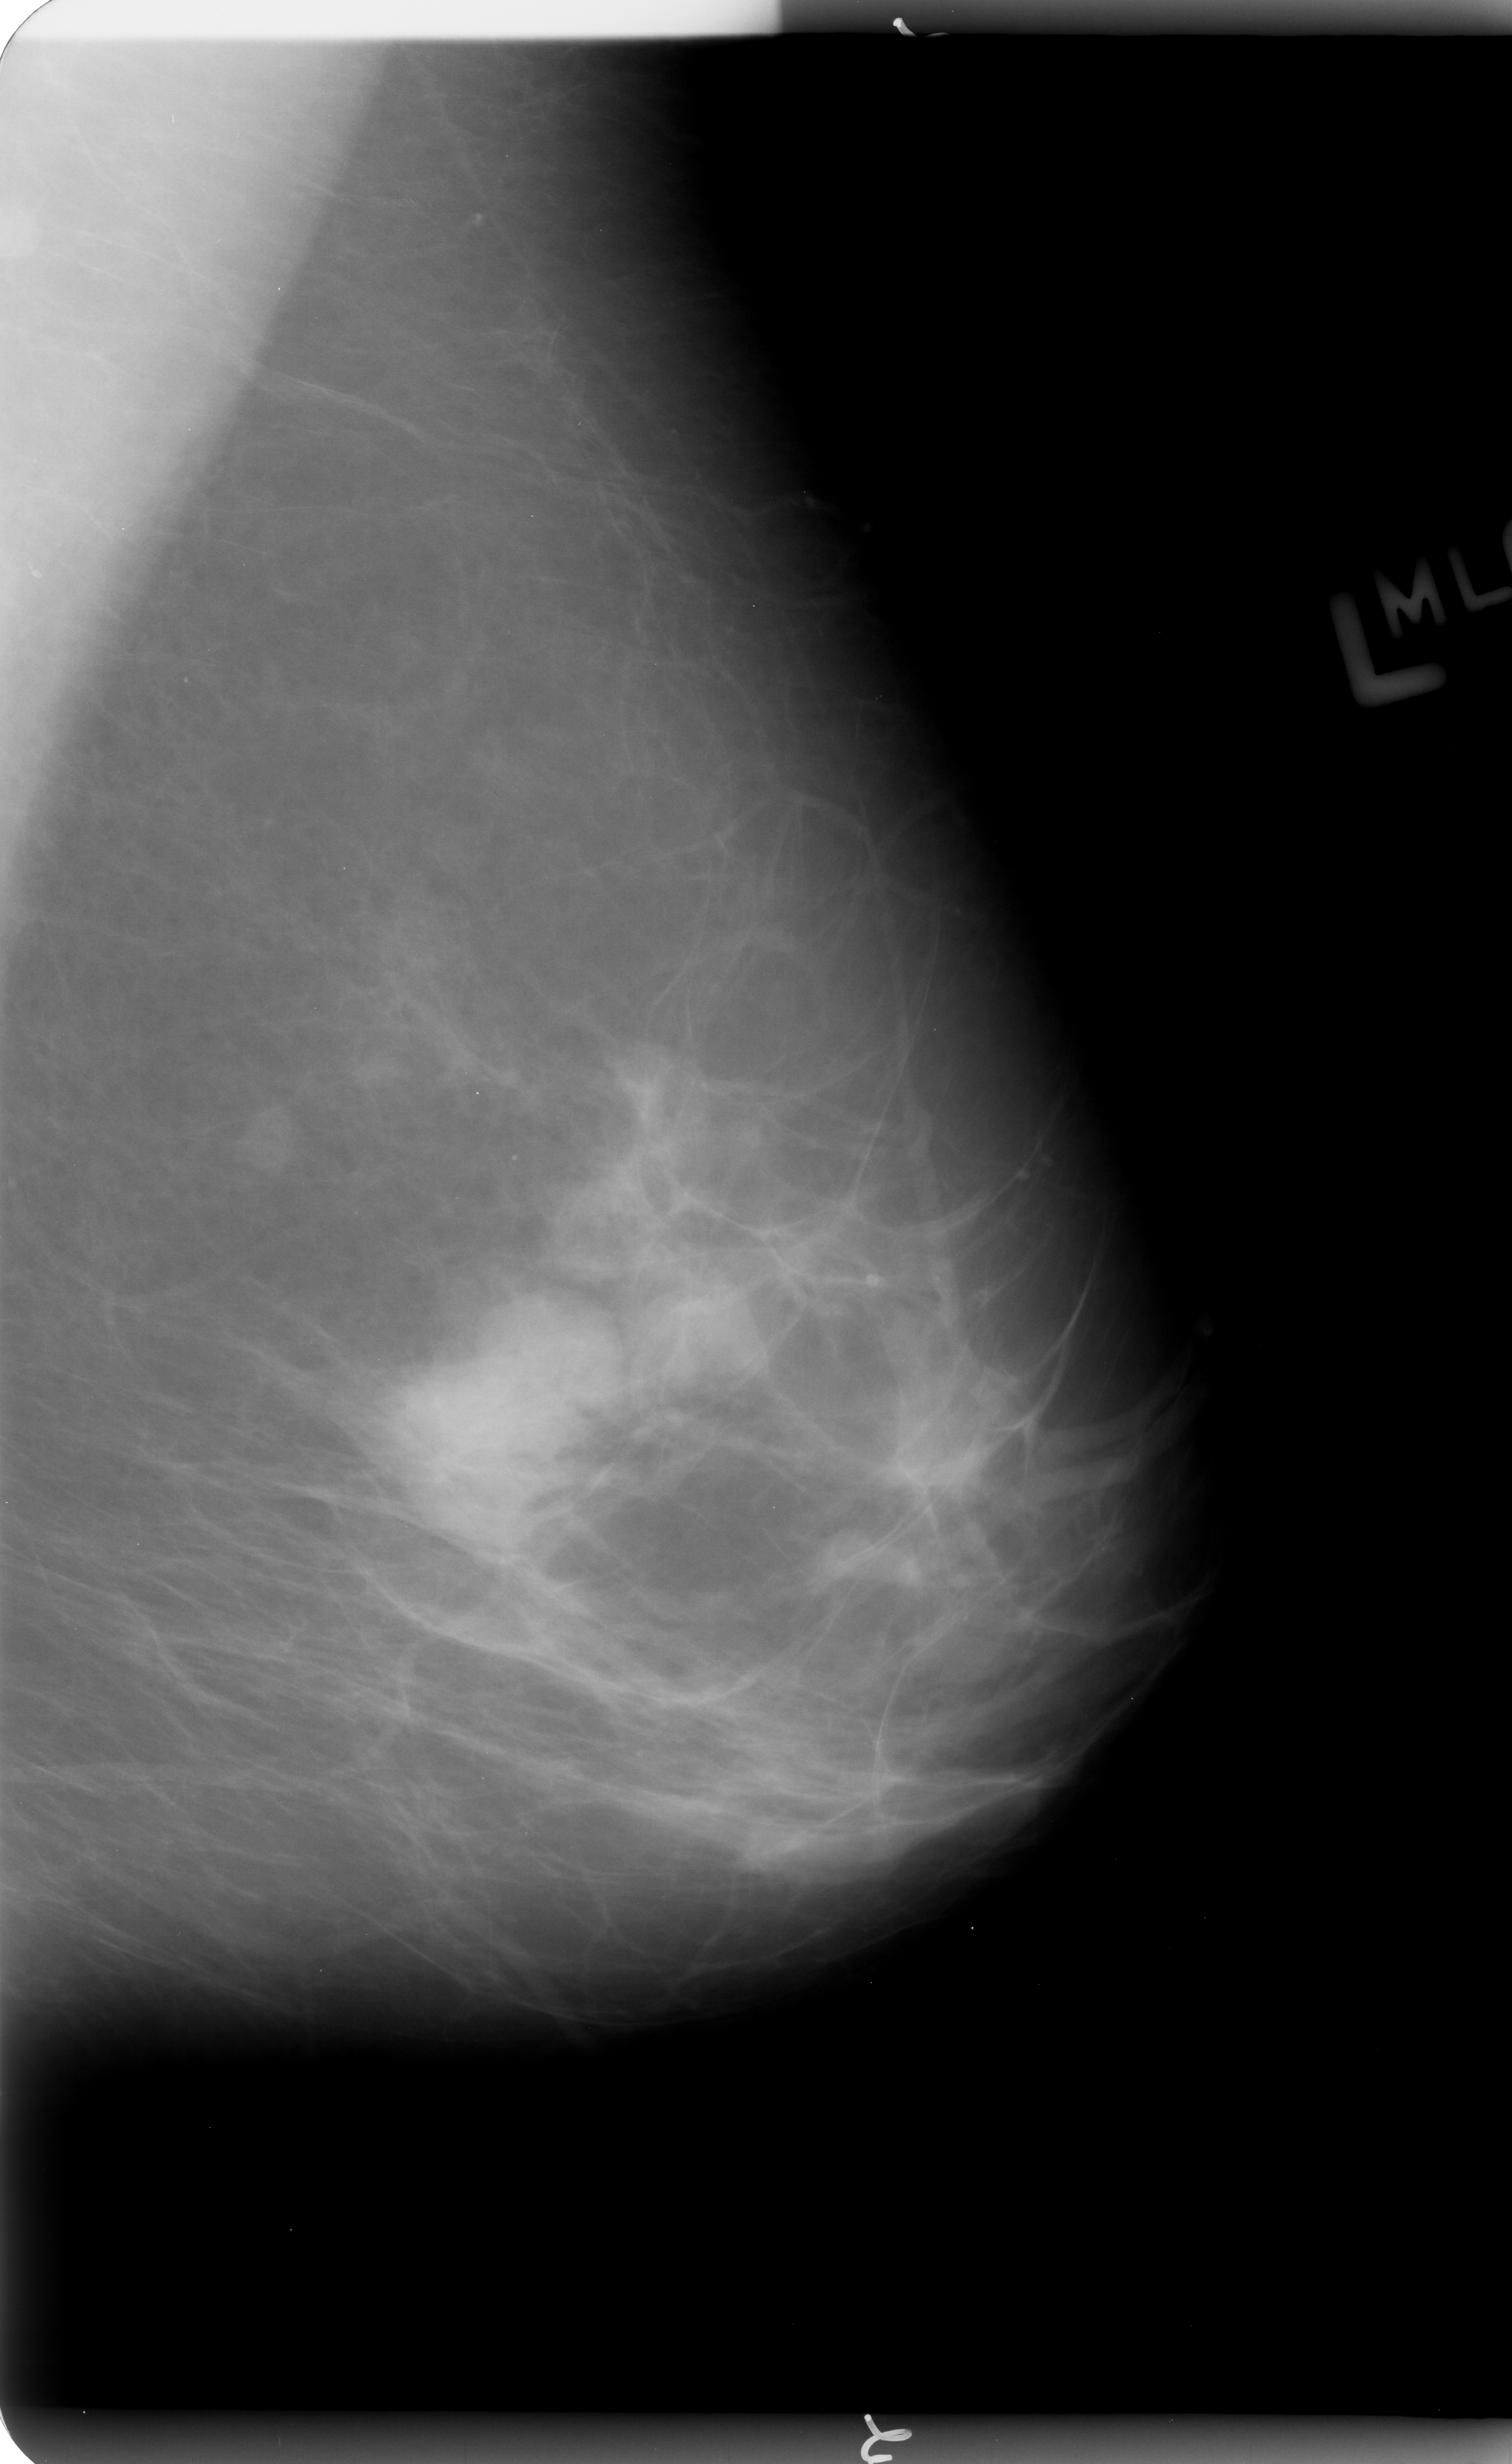
Scanned film-screen mammogram, left breast, MLO view, BI-RADS breast density category 2 (scale 1–4).
- Radiologist-marked abnormalities on this image: mass, shape lobulated, margins circumscribed / ill defined; BI-RADS assessment category 4; pathology (as recorded): benign.